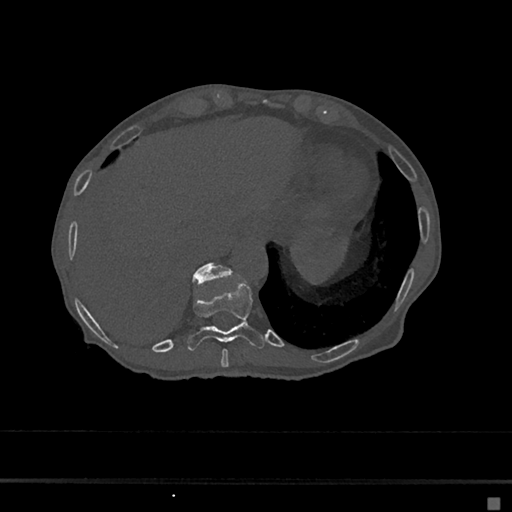
CT including the spine, one axial slice; position 223 of 797 along the scan axis; reconstruction kernel Br40s/3; 120 kVp; bone window (W 1800 / L 400 HU); 0.5 mm slice thickness; 512 × 512 image matrix. Female patient, age 68 years. Case-level facts recorded for this patient, not image findings: primary cancer: renal.
Outlined on this slice (semi-automatically segmented with operator editing):
- T10 vertebra: box from (x=187, y=281) to (x=264, y=351) px
- T11 vertebra: (x=192, y=263)–(x=231, y=285)
- T9 vertebra: (x=221, y=349)–(x=229, y=367)